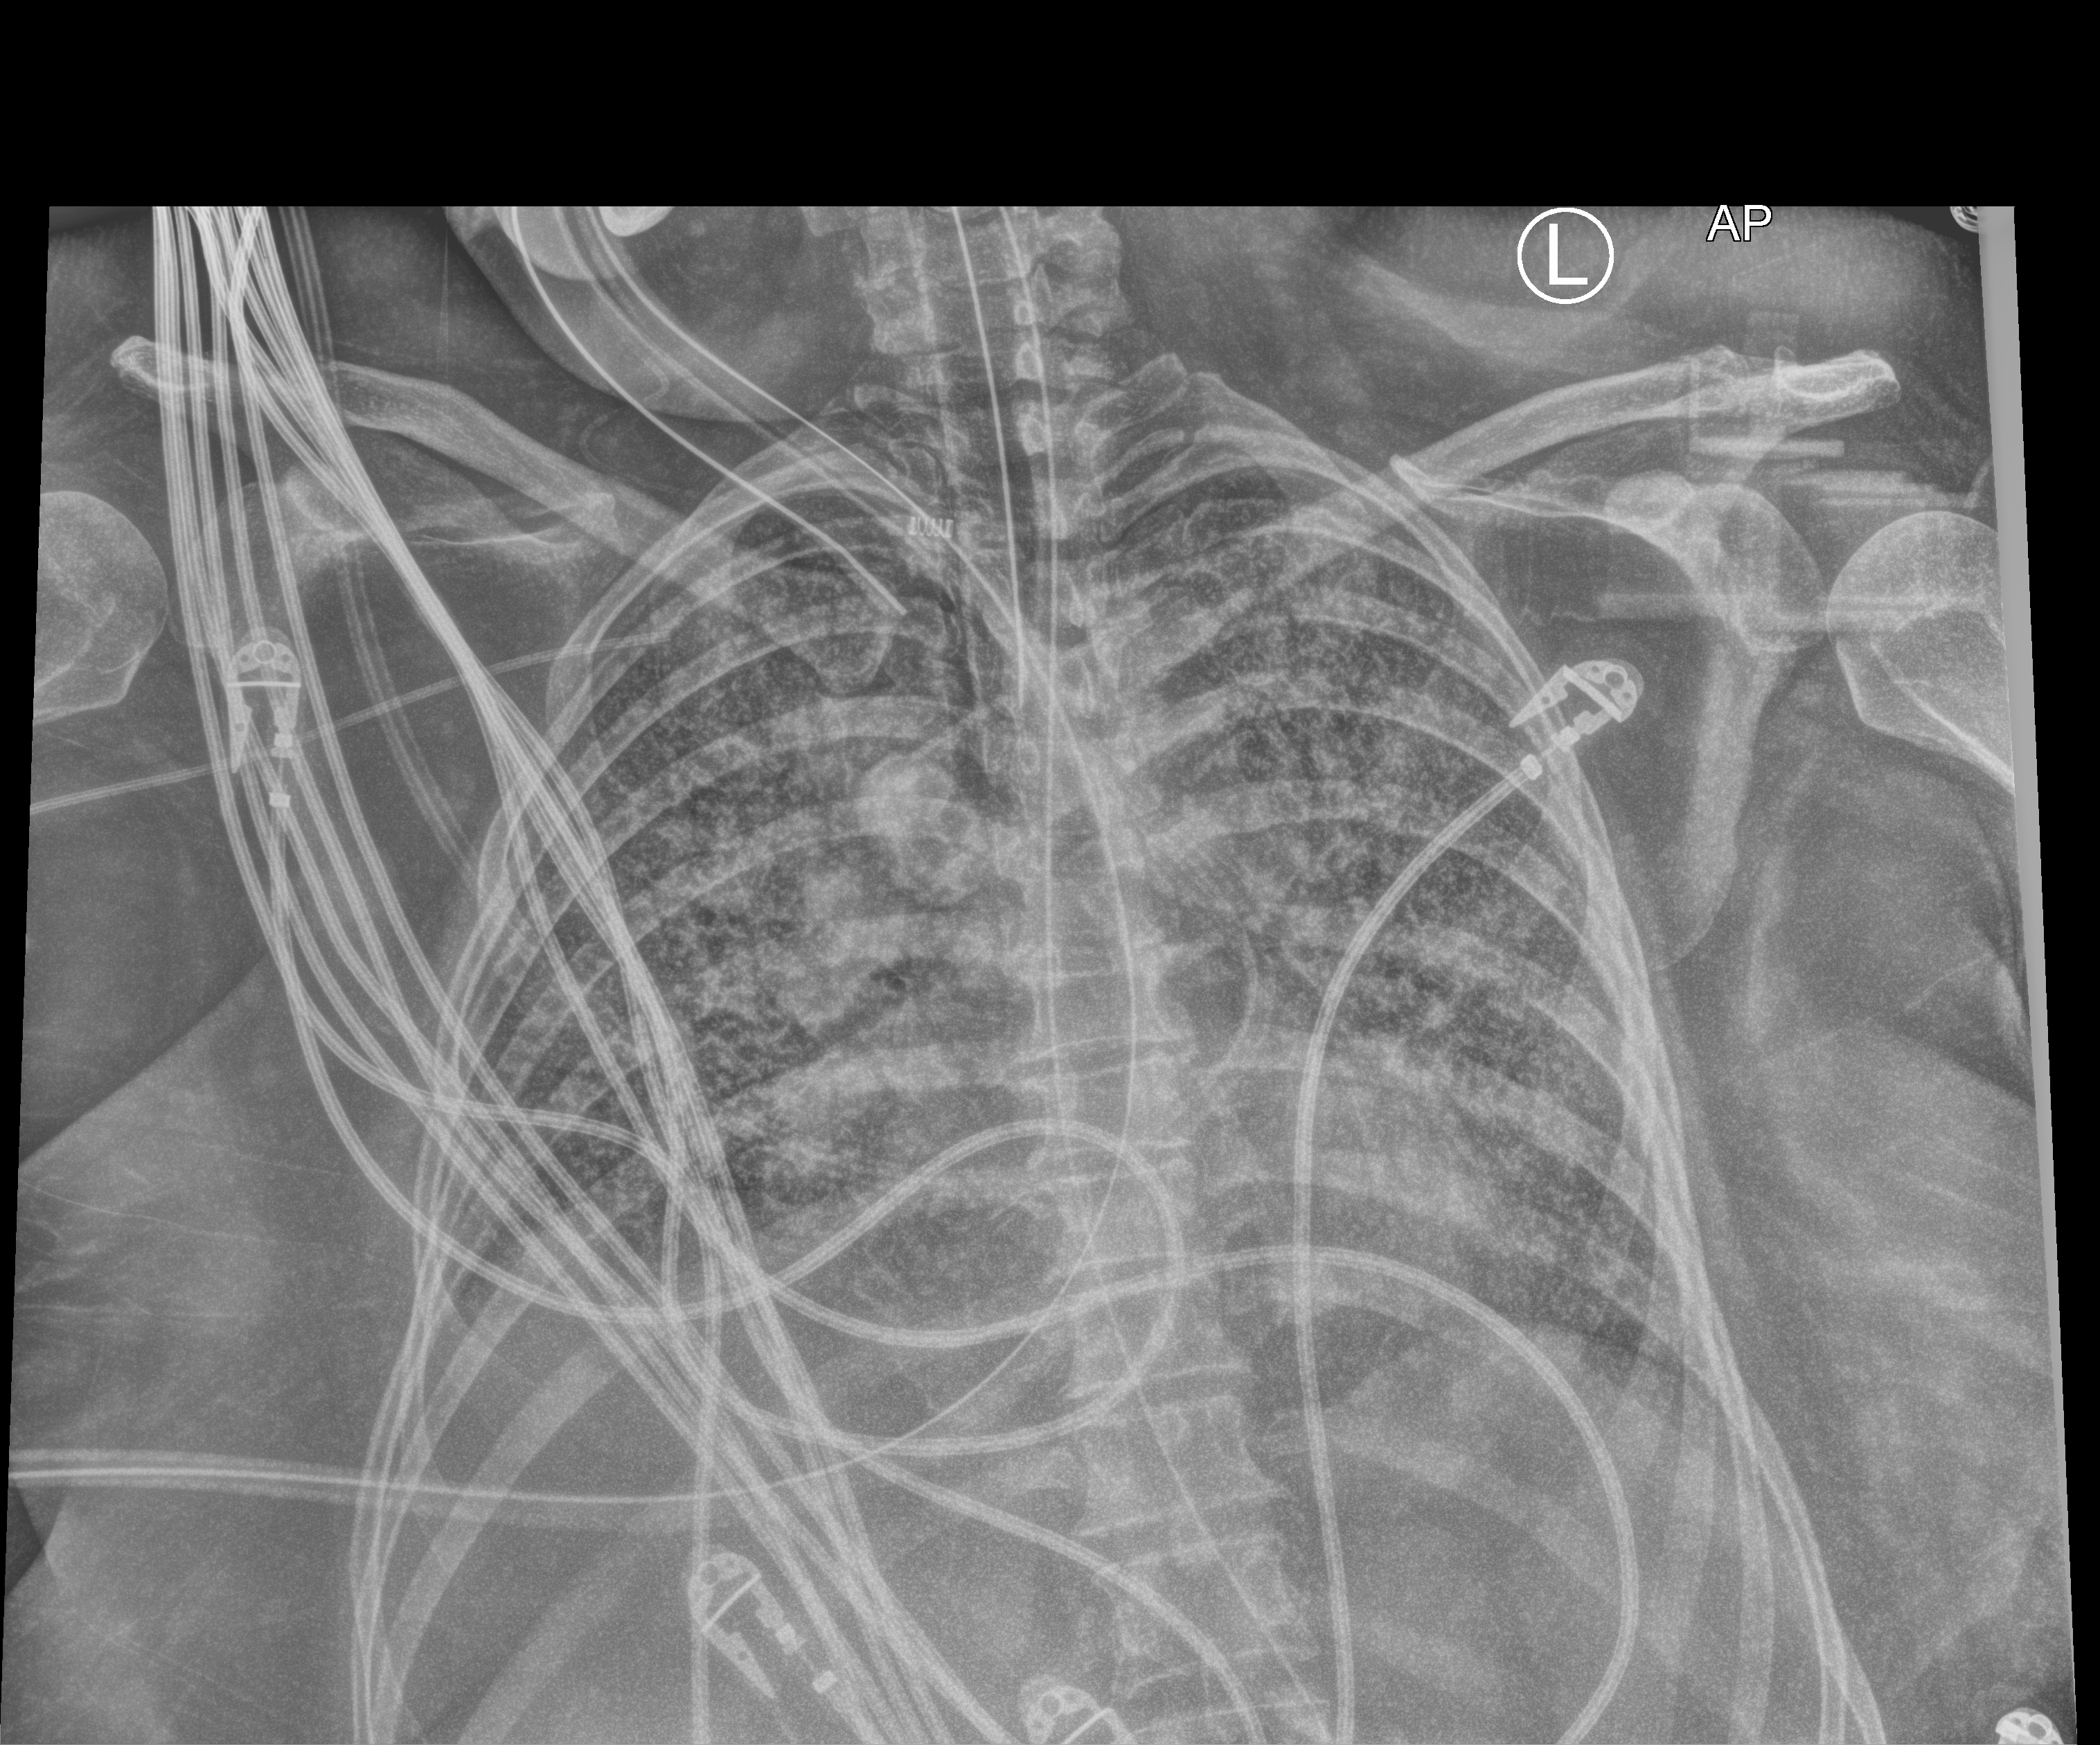
Portable chest radiograph, anteroposterior (AP) projection. Female patient hospitalised with COVID-19, age 18–59 years.
From the hospital-stay record, not from the radiograph (when in the stay this image was taken is not recorded):
- admitted to intensive care during this hospital stay: yes